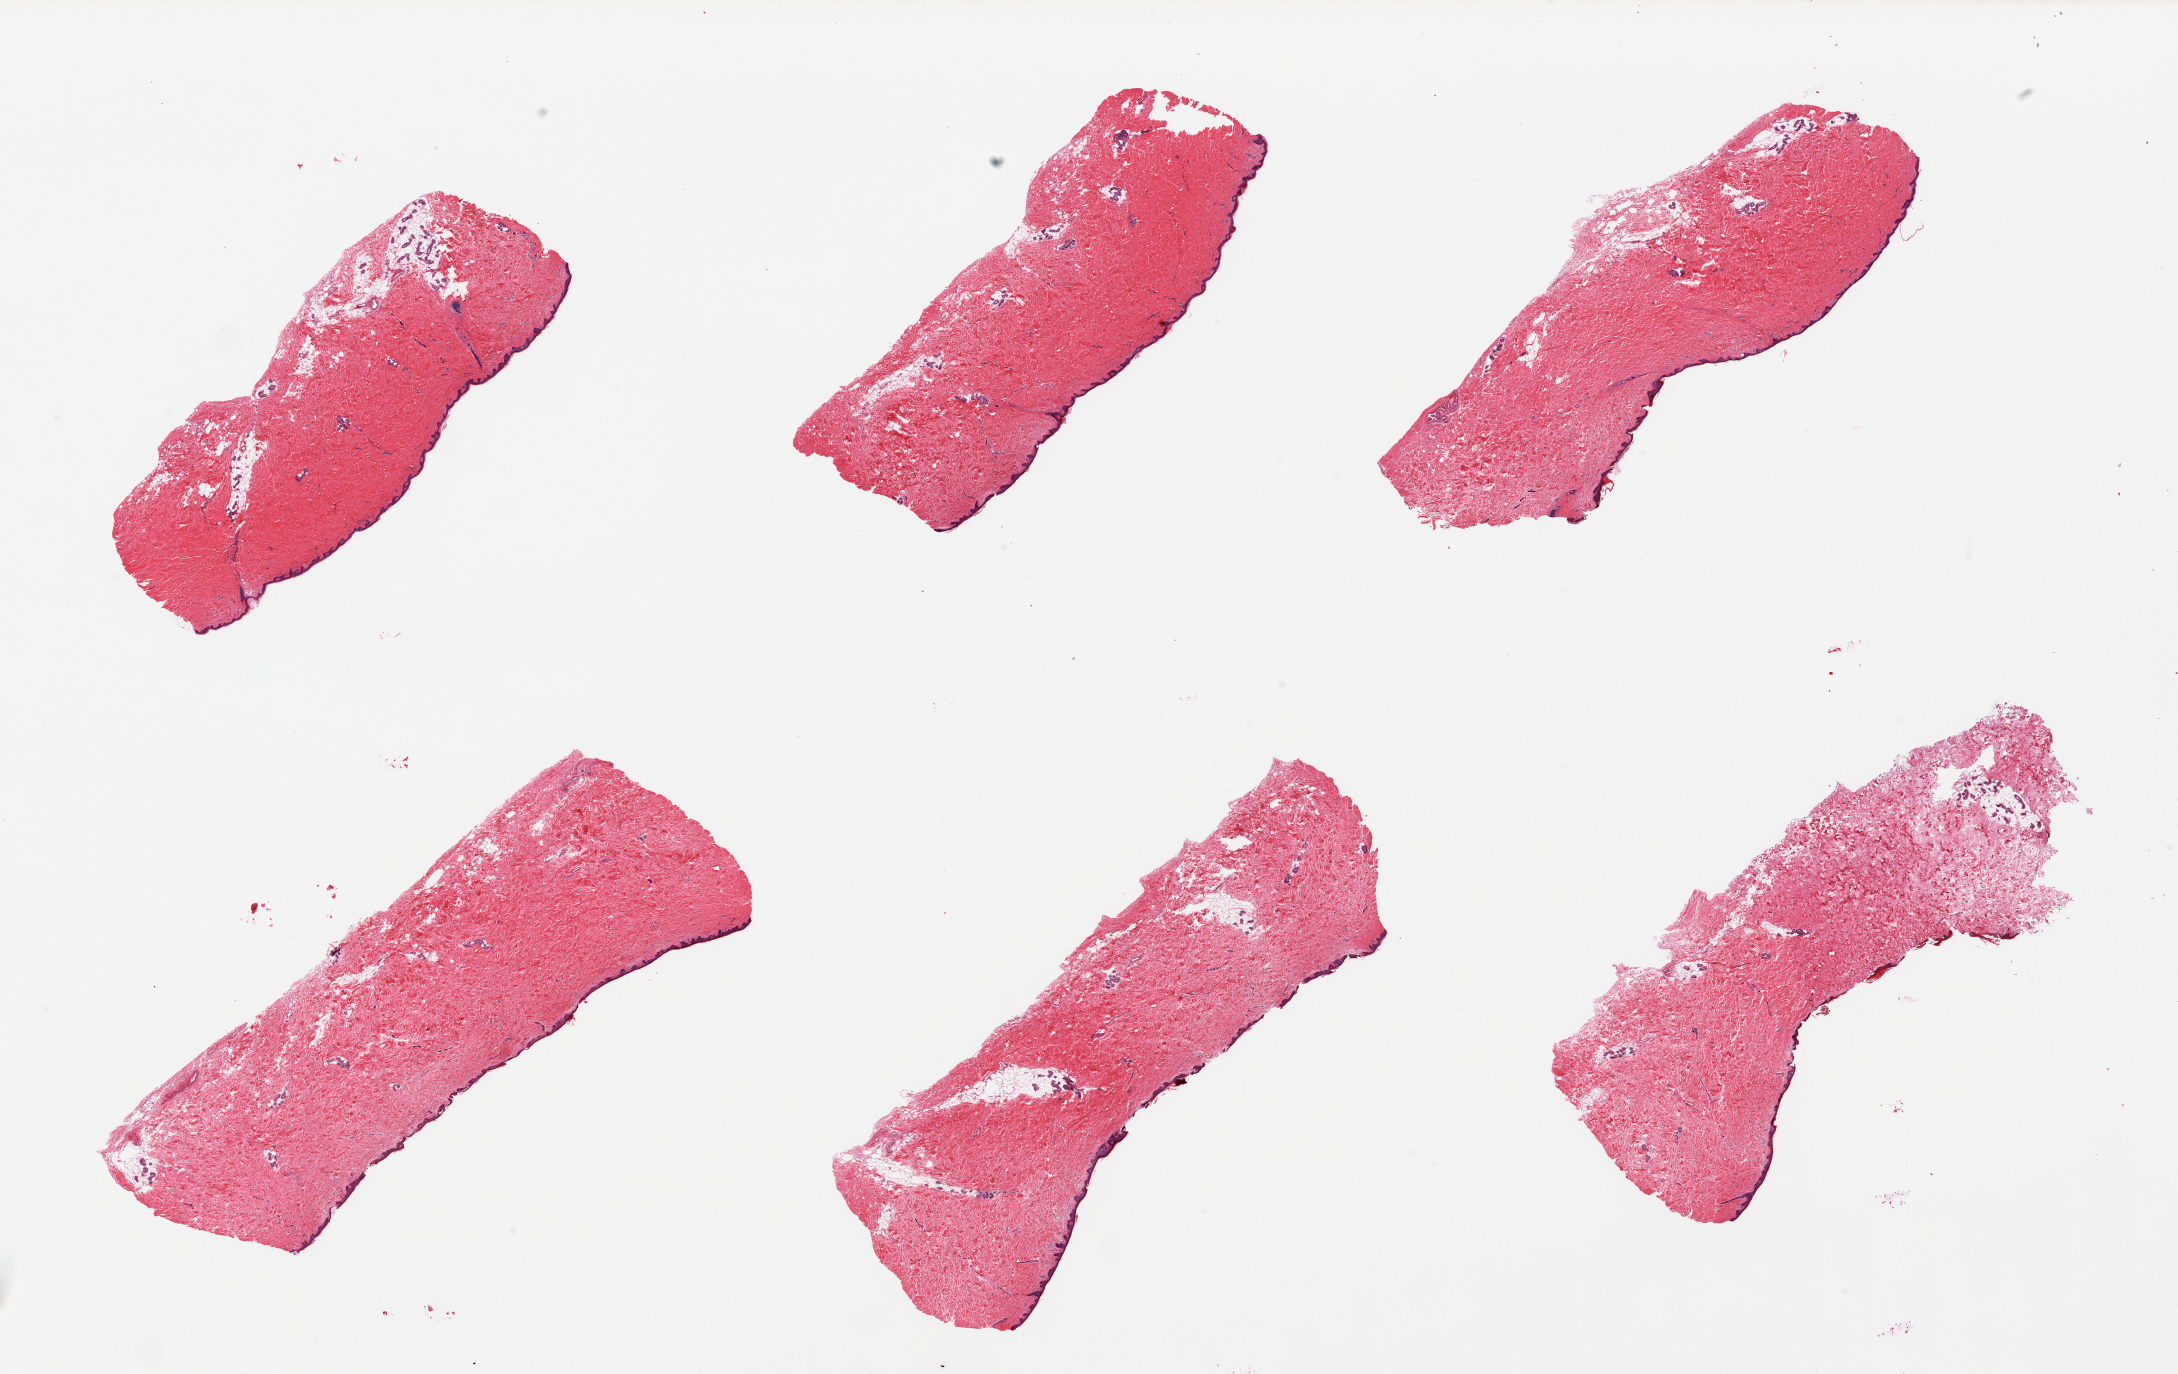
Hematoxylin and eosin (H&E) whole-slide image, shown as a low-resolution overview of the whole scanned area (about 34.5 x 21.7 mm). PAXgene-fixed paraffin-embedded (PFPE) section. Section of skin of suprapubic region (target tissue). Tissue donor sample. Donor sex: female.
• reviewer comment on this tissue sample: 6 pieces, minimal dermal fat; squamous epithelium is ~ 40-60 microns